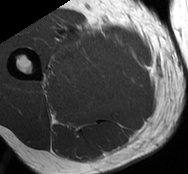
MRI of an extremity soft-tissue mass, one axial slice. Slice 24 of 93 in the series (ordered by position). MR volume resampled by the dataset authors to the PET/CT grid (not the native acquisition matrix). 3.27 mm slice thickness. 188 × 174 image matrix, field of view 184 × 170 mm. Male patient. Case-level facts recorded for this patient, not image findings: histological type: undifferentiated - pleiomorphic; grade: high; site of the primary tumour: right thigh.
Structures marked on this image (expert contour drawn on MRI and transferred to this co-registered scan by the dataset authors):
- gross tumour volume including surrounding oedema: bounding box (x1, y1, x2, y2) in pixels: (47, 28, 126, 82)